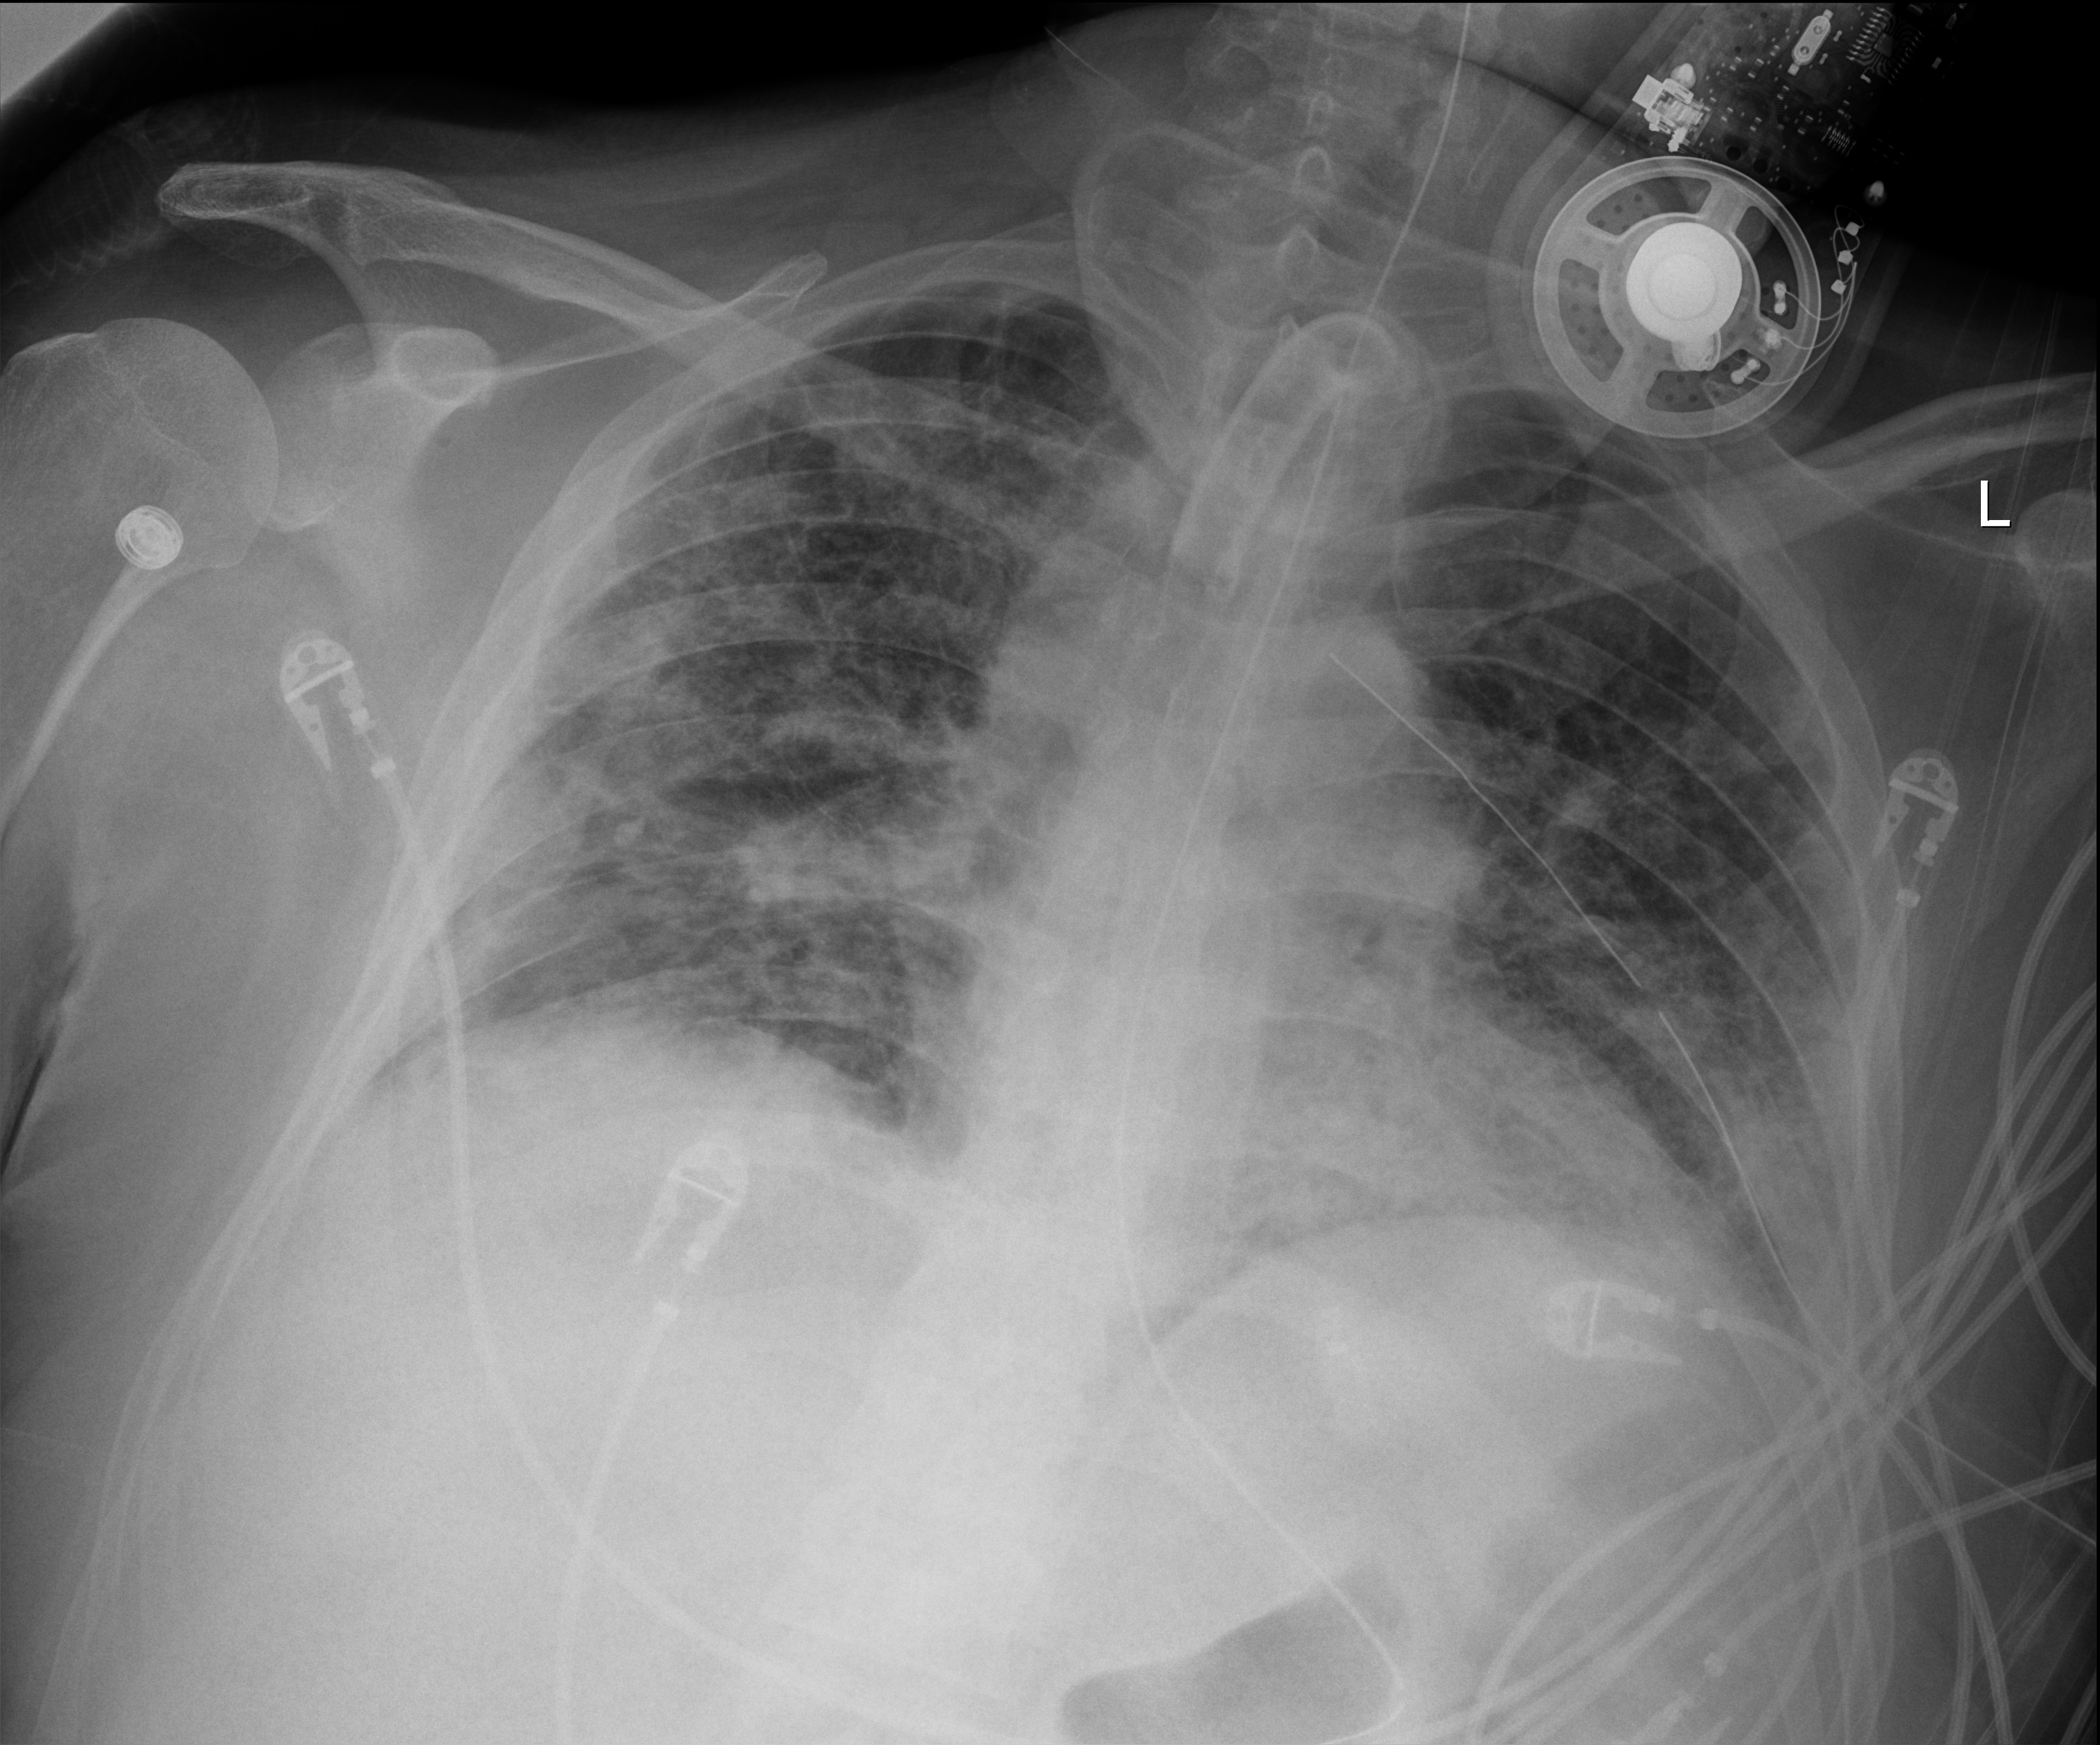
Chest X-ray; anteroposterior (AP) projection. Patient hospitalised with COVID-19; male, aged 18–59 years.
Hospital-stay facts (about this admission, not read from this image; timing relative to this image not recorded):
- length of hospital stay: 63 days
- mechanically ventilated during this hospital stay: yes
- admitted to intensive care during this hospital stay: yes